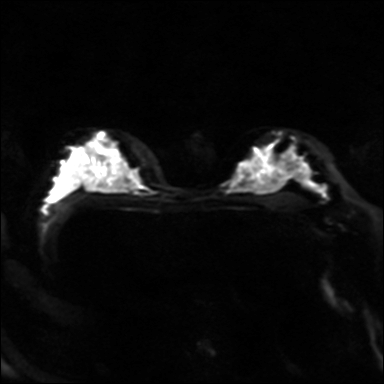
Breast MRI, one axial slice; slice 26 of 40 in the series (ordered by position); diffusion-weighted series; image 2 of 4 stored at this slice position (different b-values; order by instance number); 3 T; 384 × 384 image matrix, field of view 320 × 320 mm. Female patient.
Structures marked on this image (outlined manually by an expert reader):
- tumour on diffusion-weighted imaging: bounding box [x1, y1, x2, y2] px = [98, 133, 103, 138]